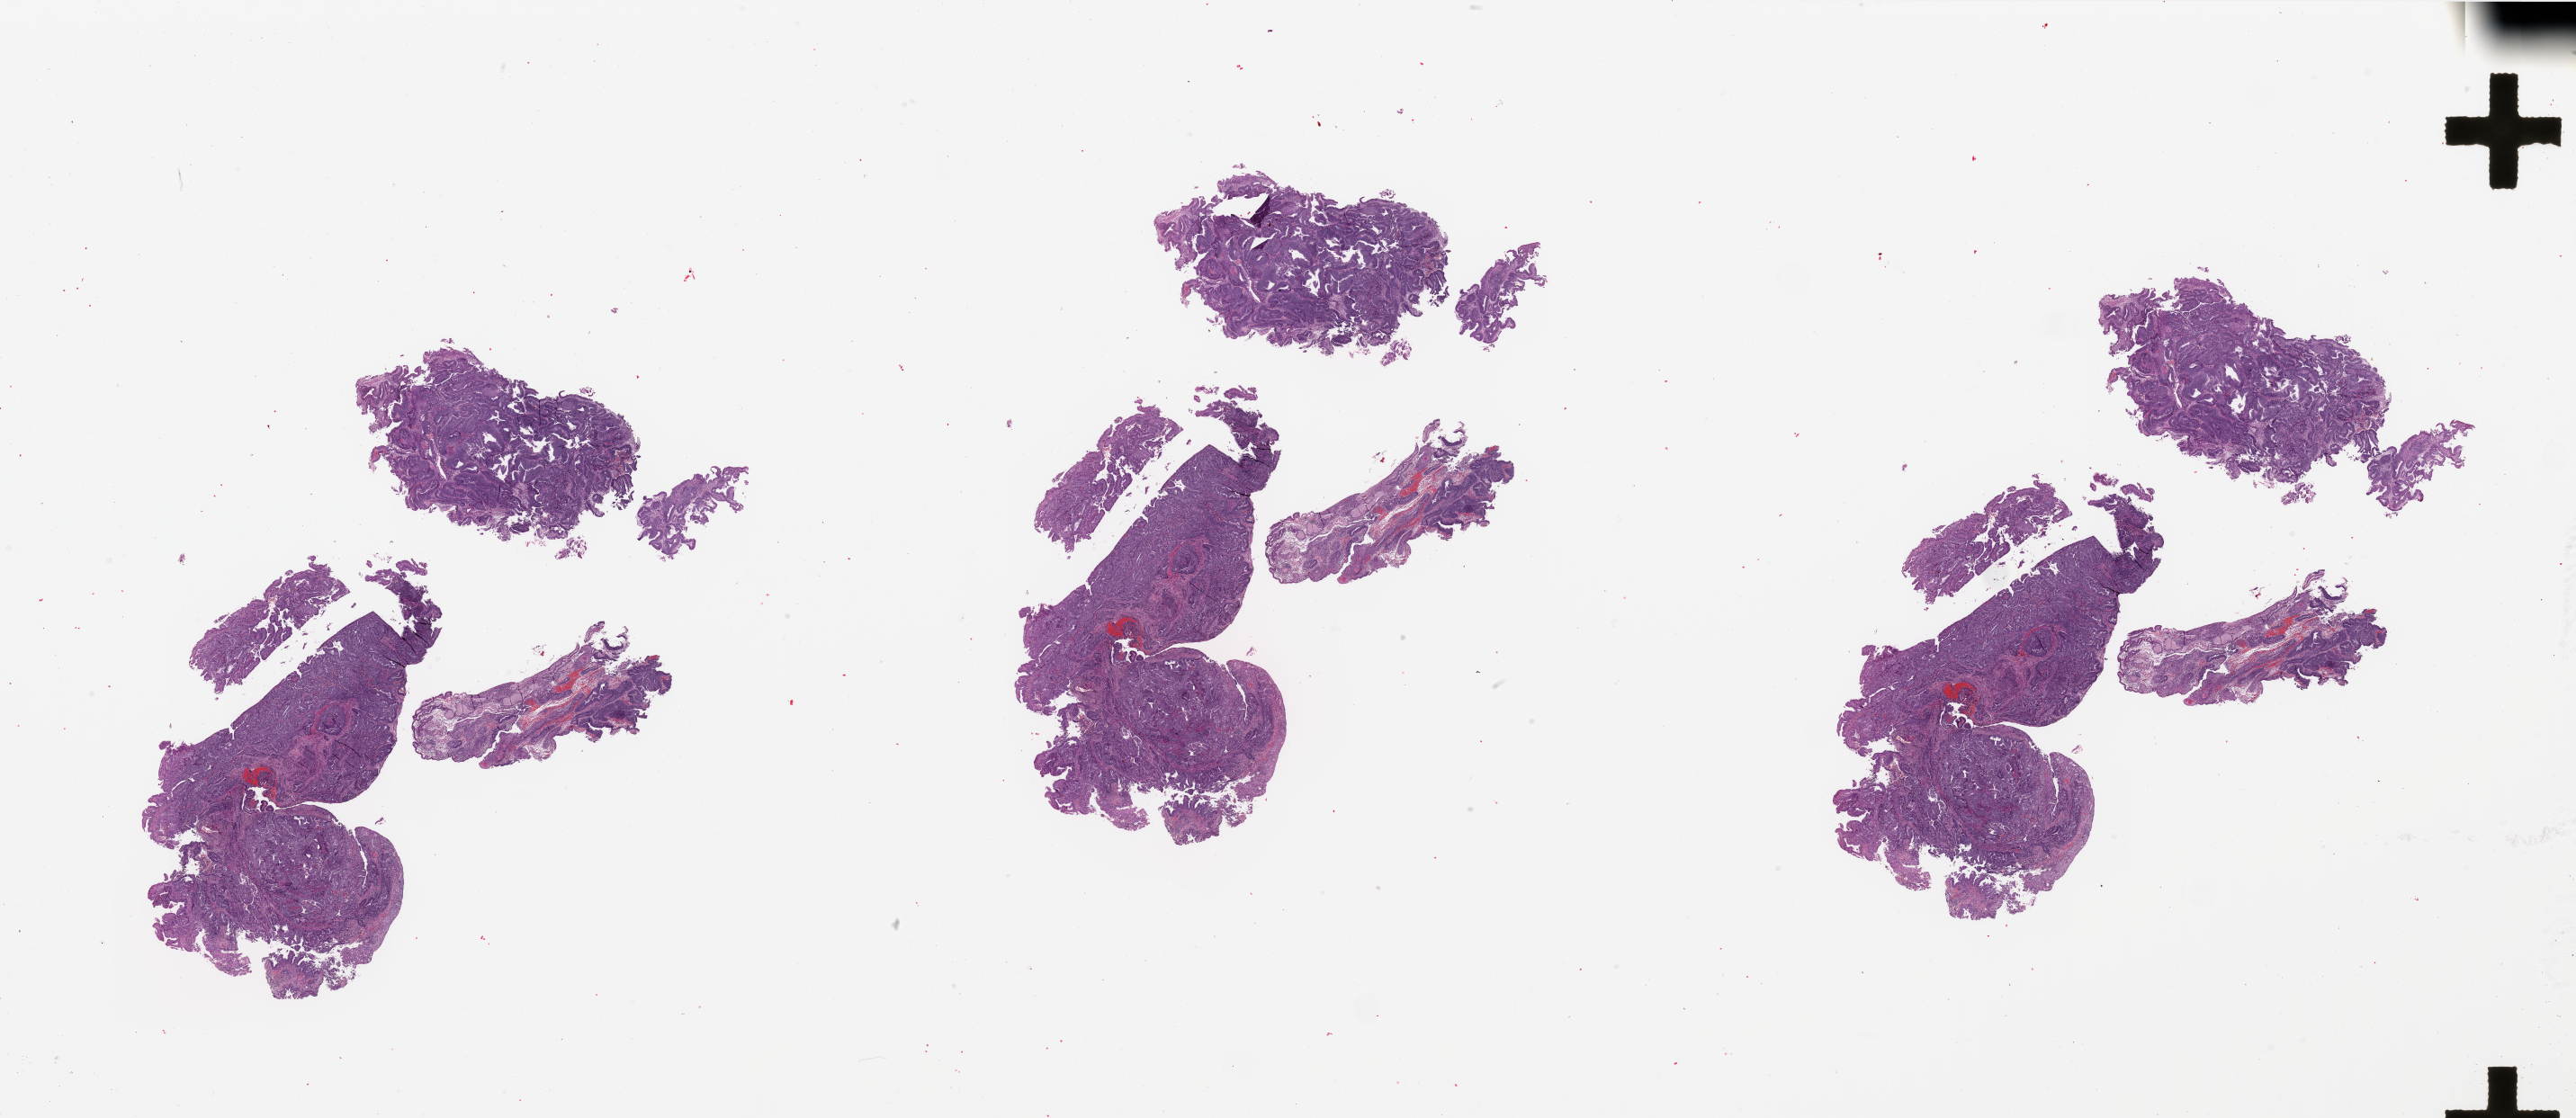
Digitized H&E tissue section (whole slide), whole scanned area (about 45.3 x 19.7 mm, acquisition: 20x scan) shown as a low-resolution overview. Tumour tissue sample, sampled site: uterus. Female, 39 y/o. Histologic grade: G2 (moderately differentiated). Pathologist review of this section (percent, as recorded): tumour nuclei 90%, necrosis 0%.
• AJCC pathologic stage: I
• diagnosis: Endometrioid adenocarcinoma, NOS